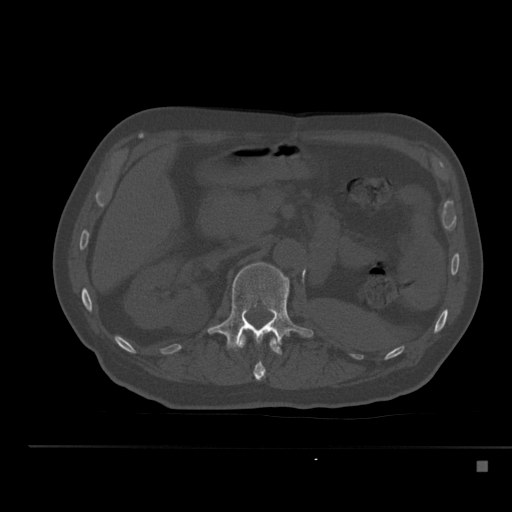
CT including the spine, one axial slice. Position 210 of 517 along the scan axis. Reconstruction kernel Br40s. 120 kVp. Bone window (W 1800 / L 400 HU). 1.5 mm slice thickness. 512 × 512 image matrix, field of view 408 × 408 mm. Male patient, age 70 years. Case-level facts recorded for this patient, not image findings: primary cancer: renal.
Outlined on this slice (semi-automatic segmentation, software-assisted and operator-edited):
- L1 vertebra: bounding box <208,262,313,350> (left, top, right, bottom; pixels)
- T12 vertebra: <239,334,282,381>